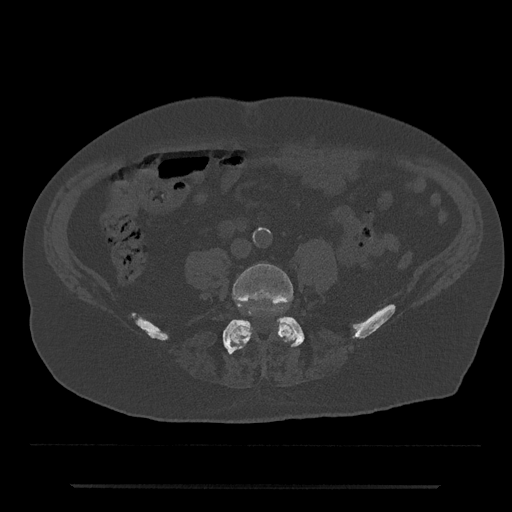
CT including the spine, one axial slice. Reconstruction kernel Br40s/3. 120 kVp. Bone window (W 1800 / L 400 HU). 0.5 mm slice thickness. 512 × 512 image matrix, field of view 434 × 434 mm. Male patient, age 80 years. Case-level facts recorded for this patient, not image findings: primary cancer: prostate.
Annotated regions visible in this slice (semi-automatically segmented with operator editing):
- L4 vertebra: bounding box <228,263,297,349> (left, top, right, bottom; pixels)
- L5 vertebra: <223,317,305,354>